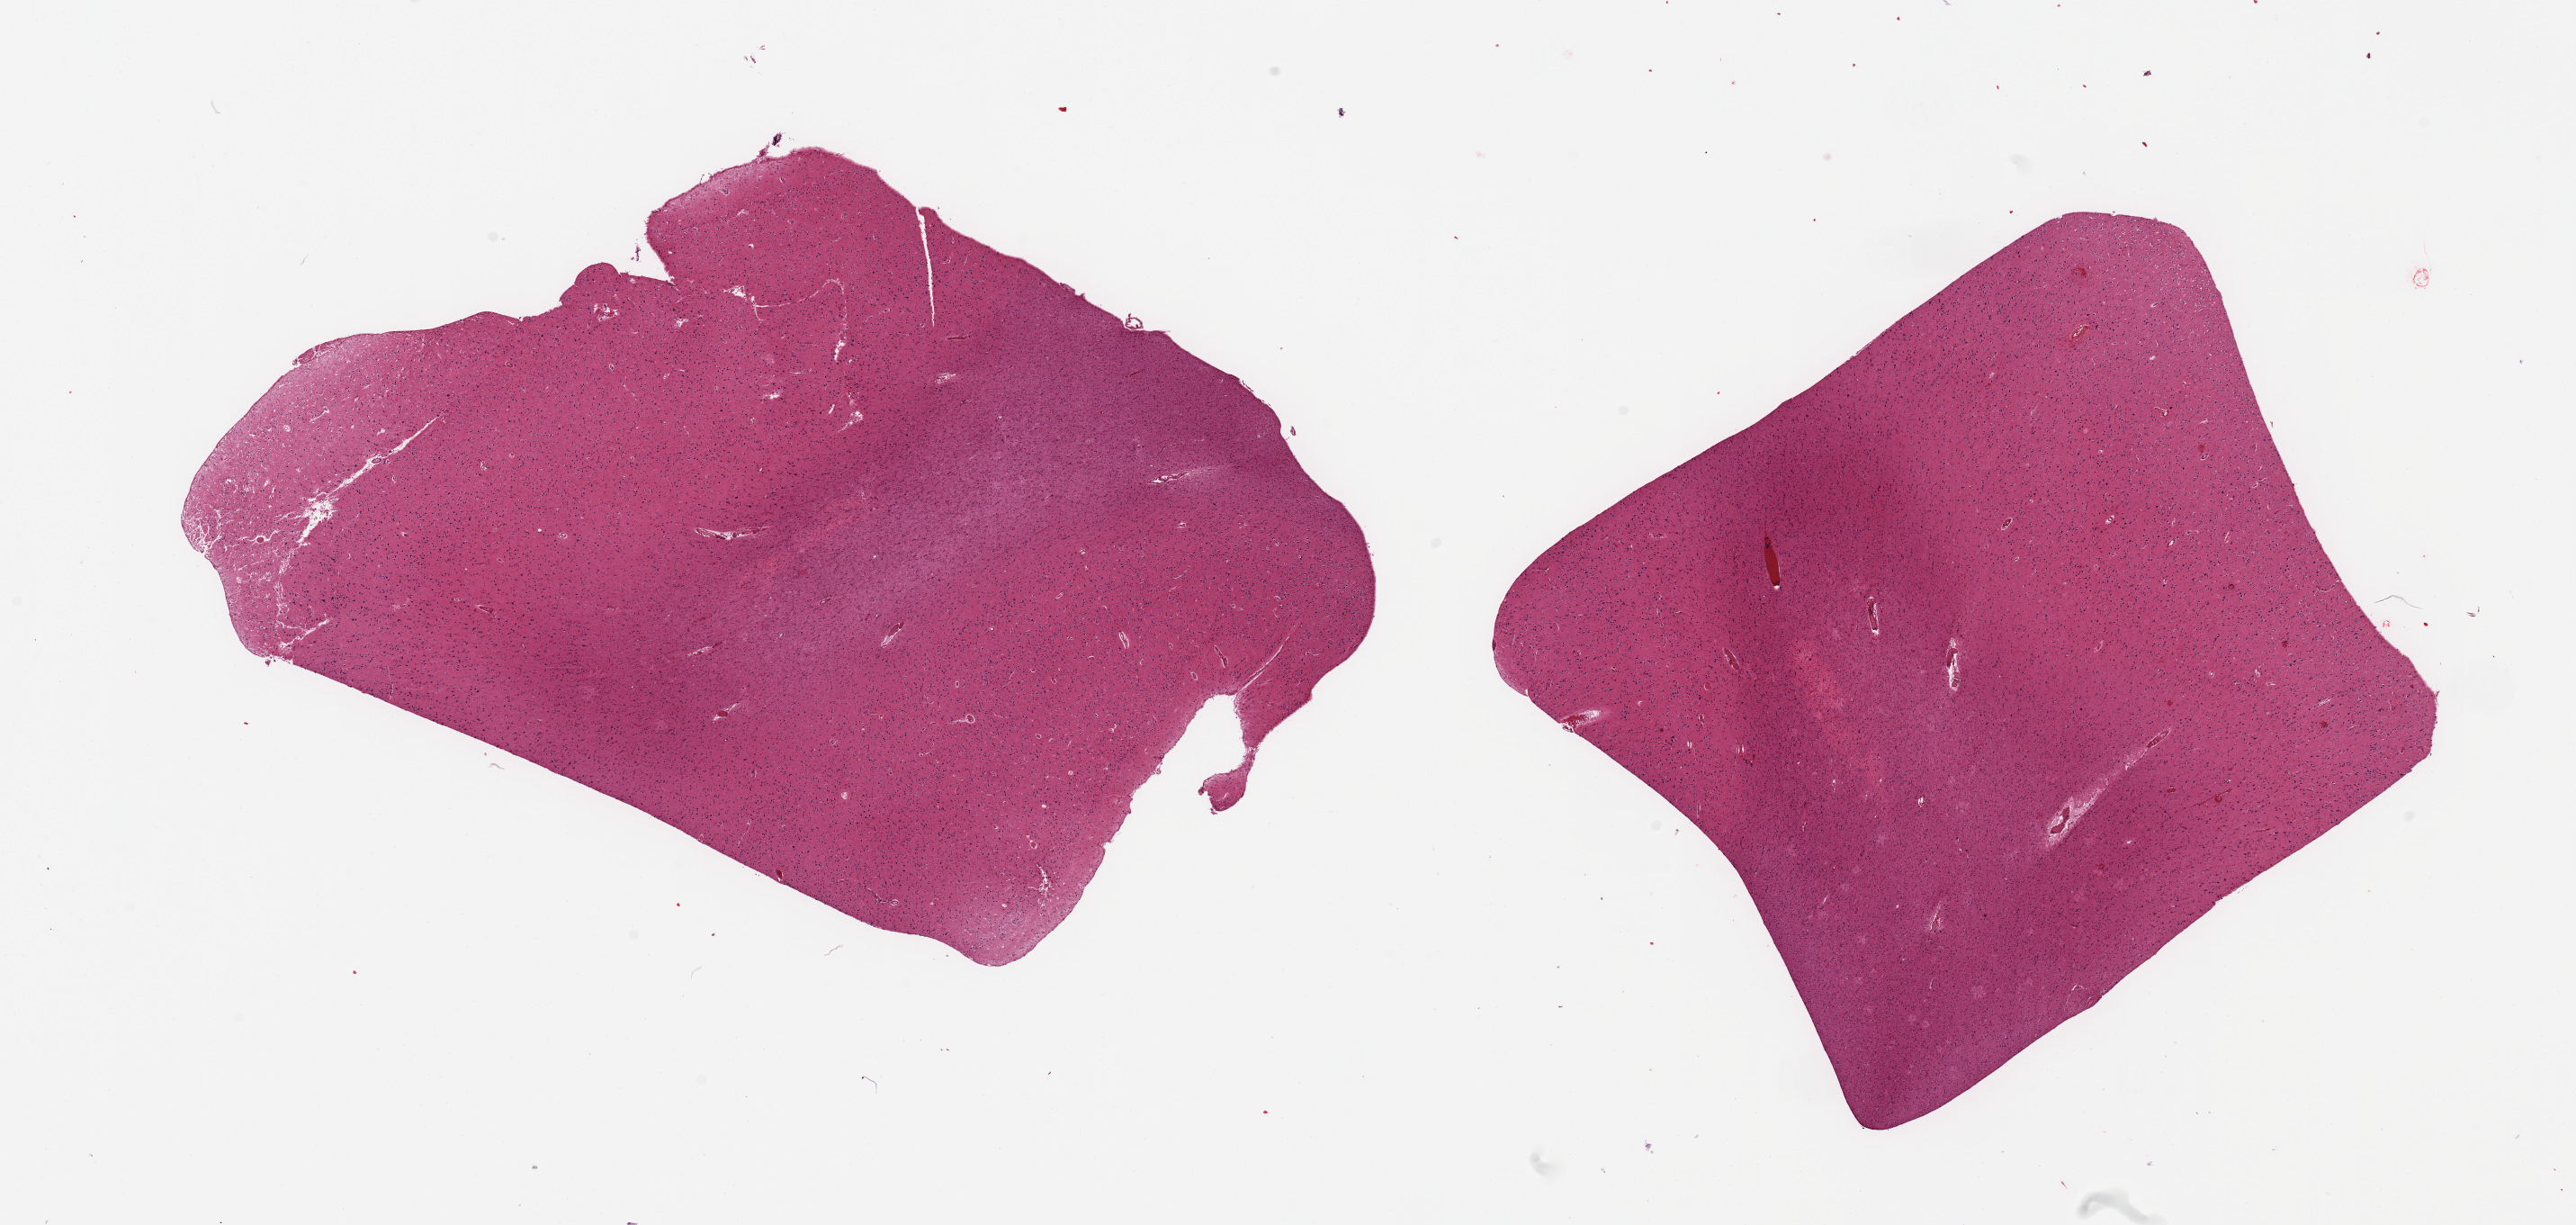
H&E whole-slide image, brightfield — shown as a low-resolution overview of the whole scanned area (about 22.6 x 10.8 mm, from a 20x scan); PAXgene-fixed paraffin-embedded (PFPE) section; sampled site (target tissue): cerebral cortex; donor tissue sample. Male donor.
- review note (as recorded): 2 pieces